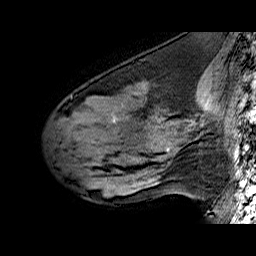
Breast MRI (dynamic contrast-enhanced), one sagittal slice. Dynamic contrast-enhanced series, time point 2 of 6 at this slice position (early post-contrast). 1.5 T. TE 6.4 ms, TR 32.9 ms. 256 × 256 image matrix, field of view 200 × 200 mm. Female patient. From the clinical record (not read from this slice): setting: breast cancer imaged before/during neoadjuvant chemotherapy; receptor status: HER2-positive.
Annotated regions visible in this slice (semi-automatic segmentation, software-assisted and operator-edited):
- analysis volume of interest (the breast-tissue region the enhancement analysis was run in; not a lesion): bounding box (x1, y1, x2, y2) in pixels: (56, 79, 196, 160)
- tumour enhancement mask (voxels above the 100 % enhancement threshold inside the analysis volume of interest): (113, 117, 170, 151)